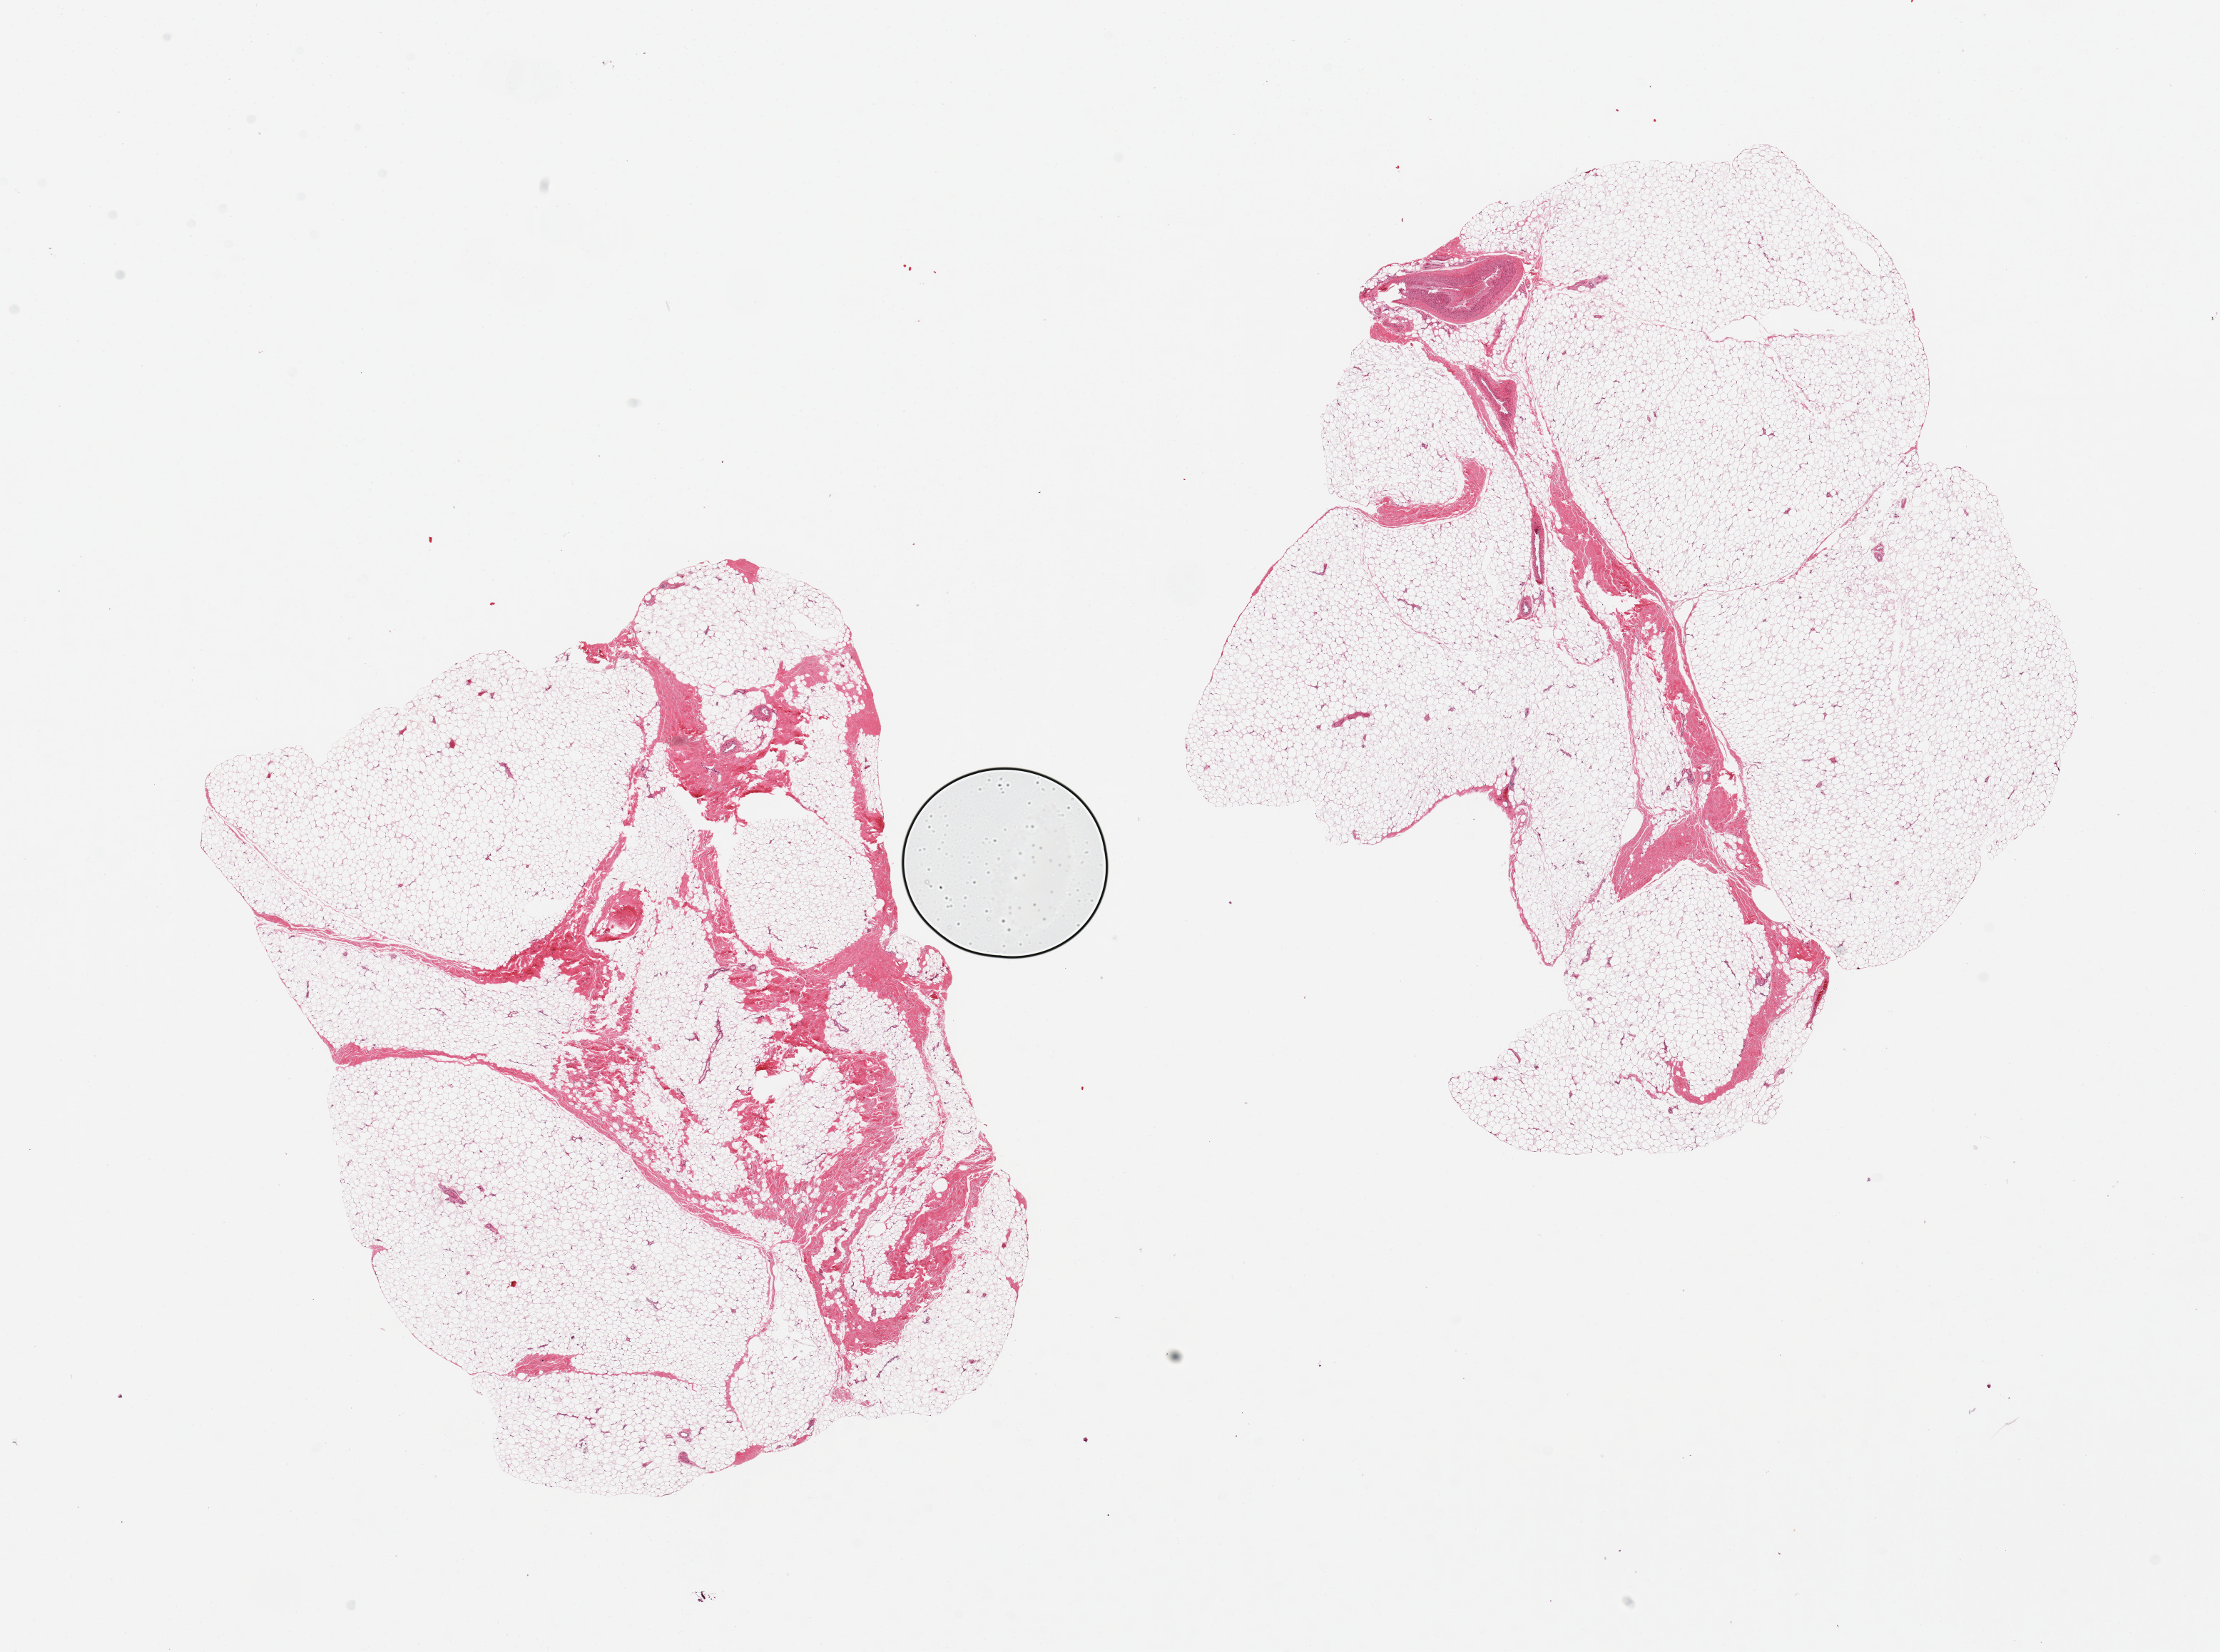
H&E whole-slide image, brightfield, whole scanned area (about 24.6 x 18.3 mm) shown as a low-resolution overview, PAXgene-fixed, paraffin-embedded tissue, section of breast (target tissue), donor tissue sample. Male donor.
Pathologist's review note for this sample: 2 pieces; mostly (90%) adipose; no ducts.